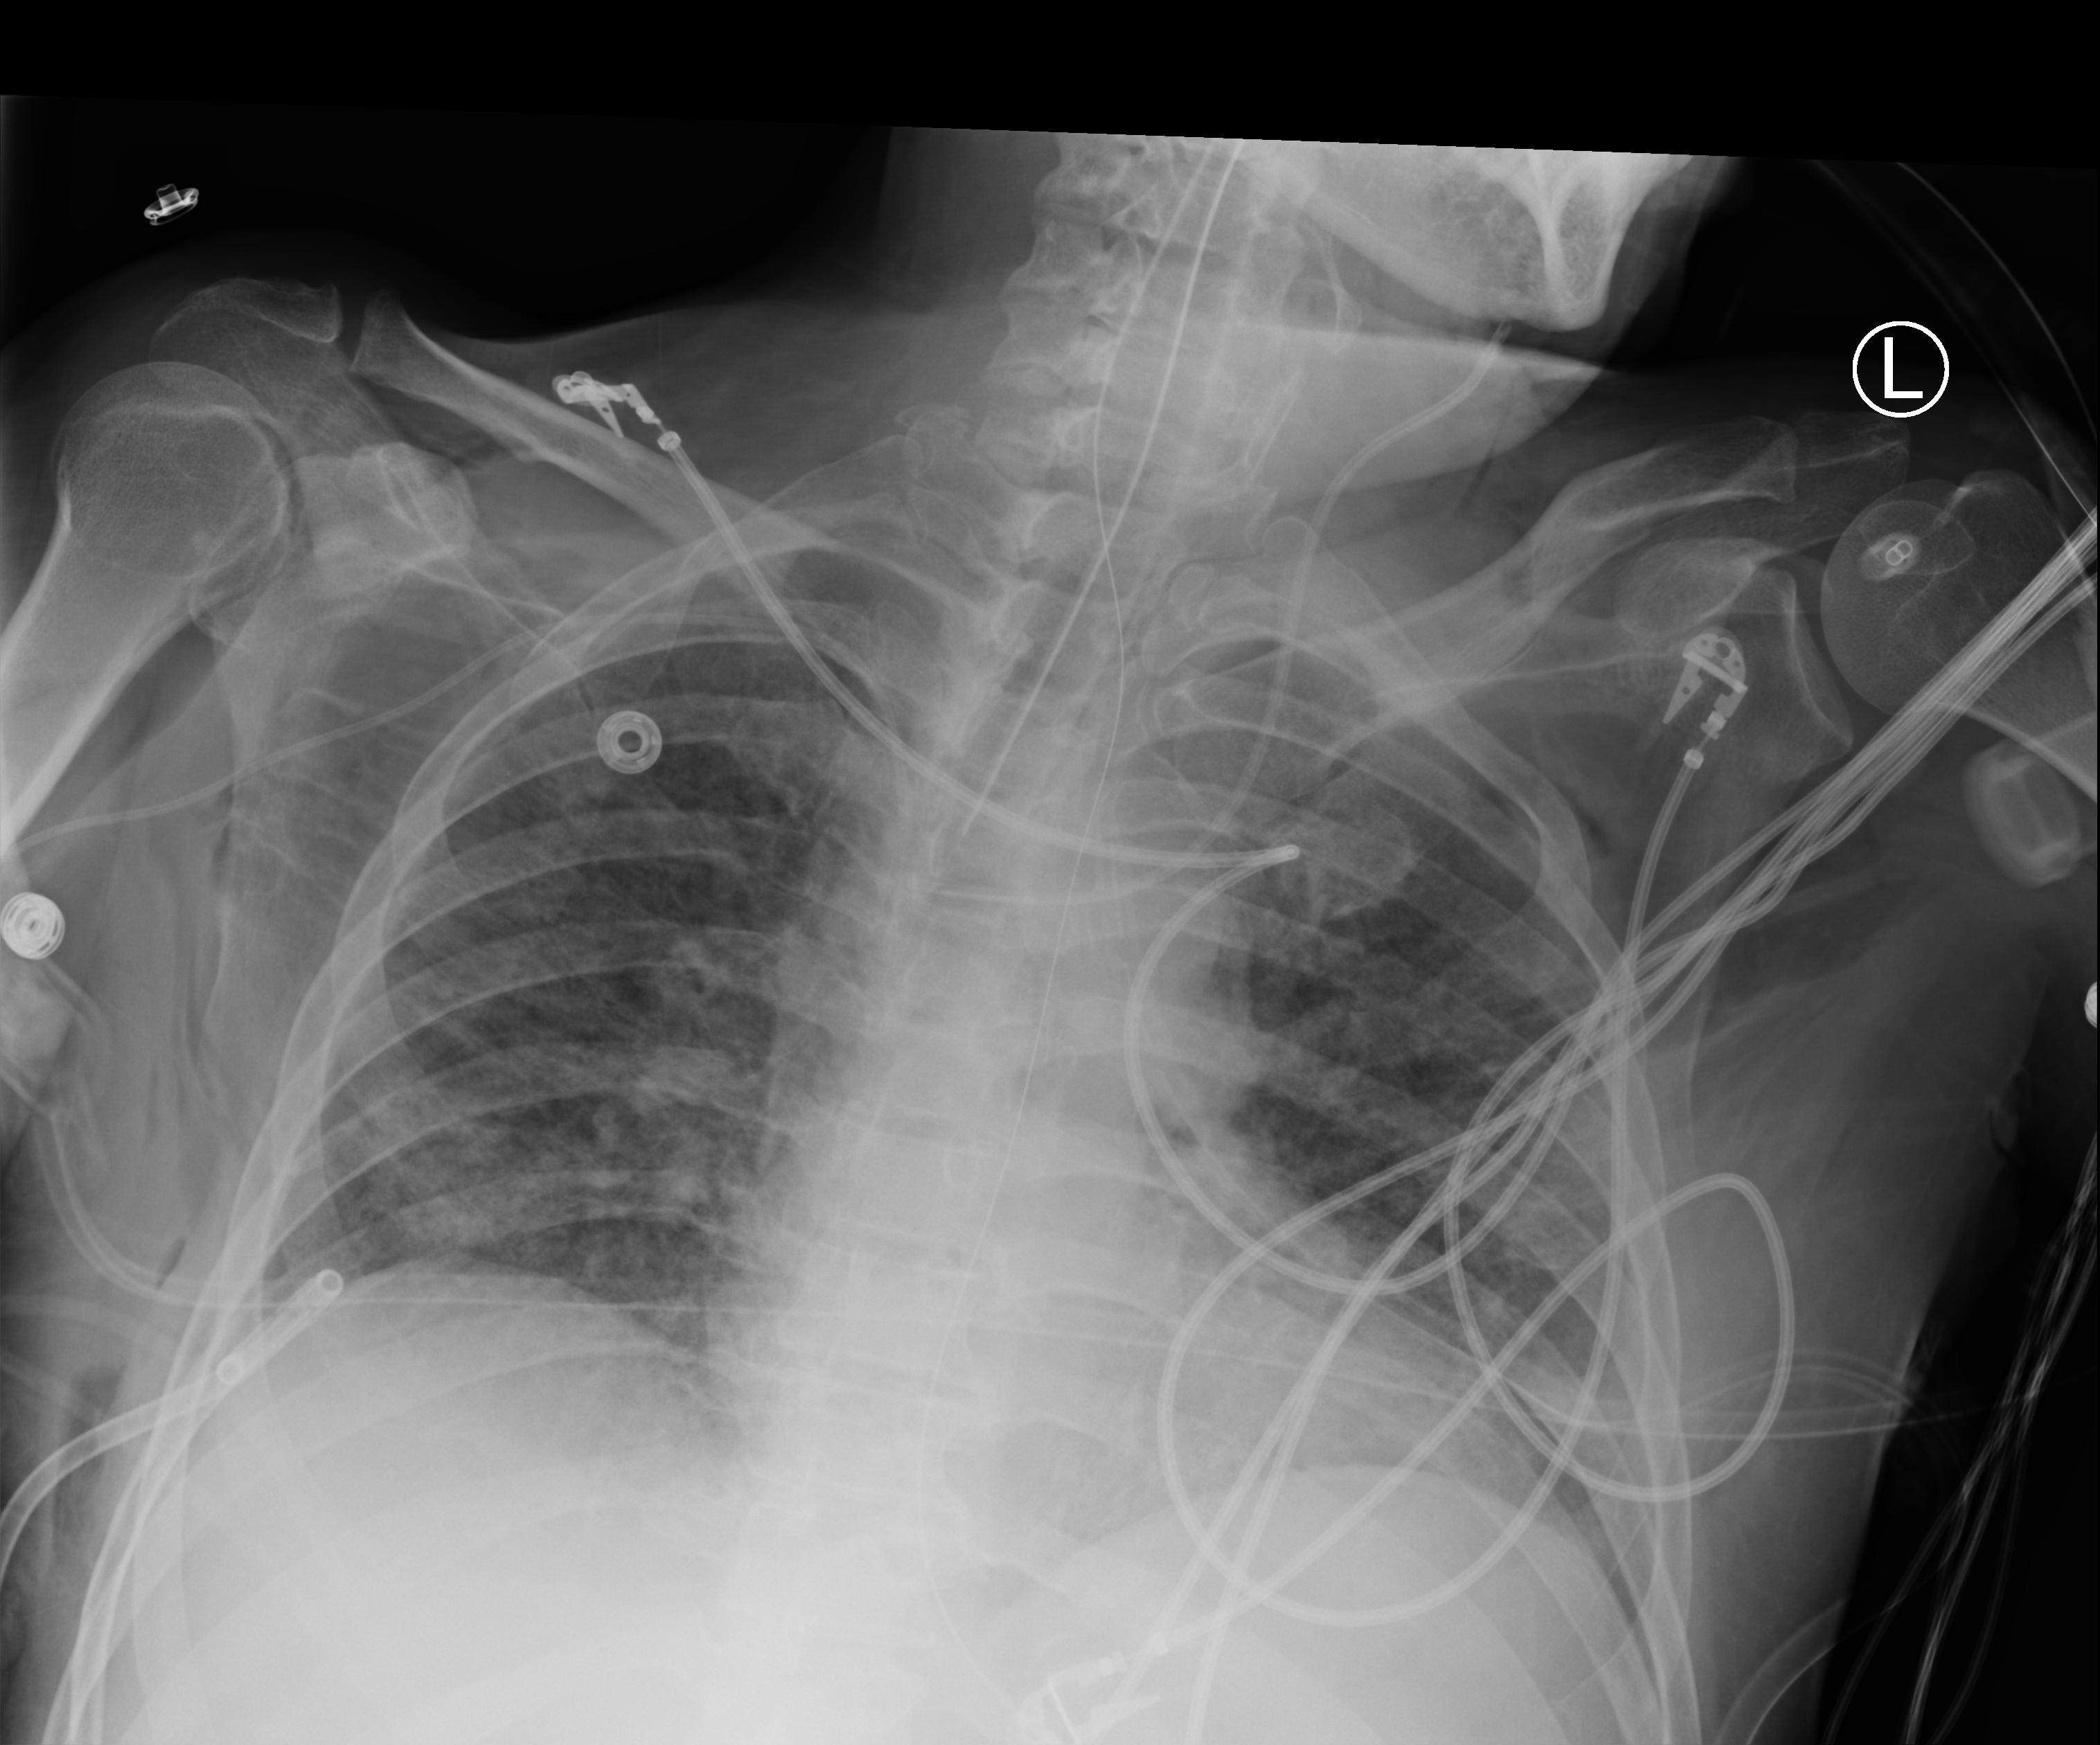
Chest X-ray (portable); anteroposterior (AP) projection. Male patient hospitalised with COVID-19, age 18–59 years.
Admission-level facts for this patient (not findings on this image; timing relative to this image not recorded):
- mechanically ventilated during this hospital stay: yes
- chronic kidney disease (admission record): no
- smoking status (admission record): never